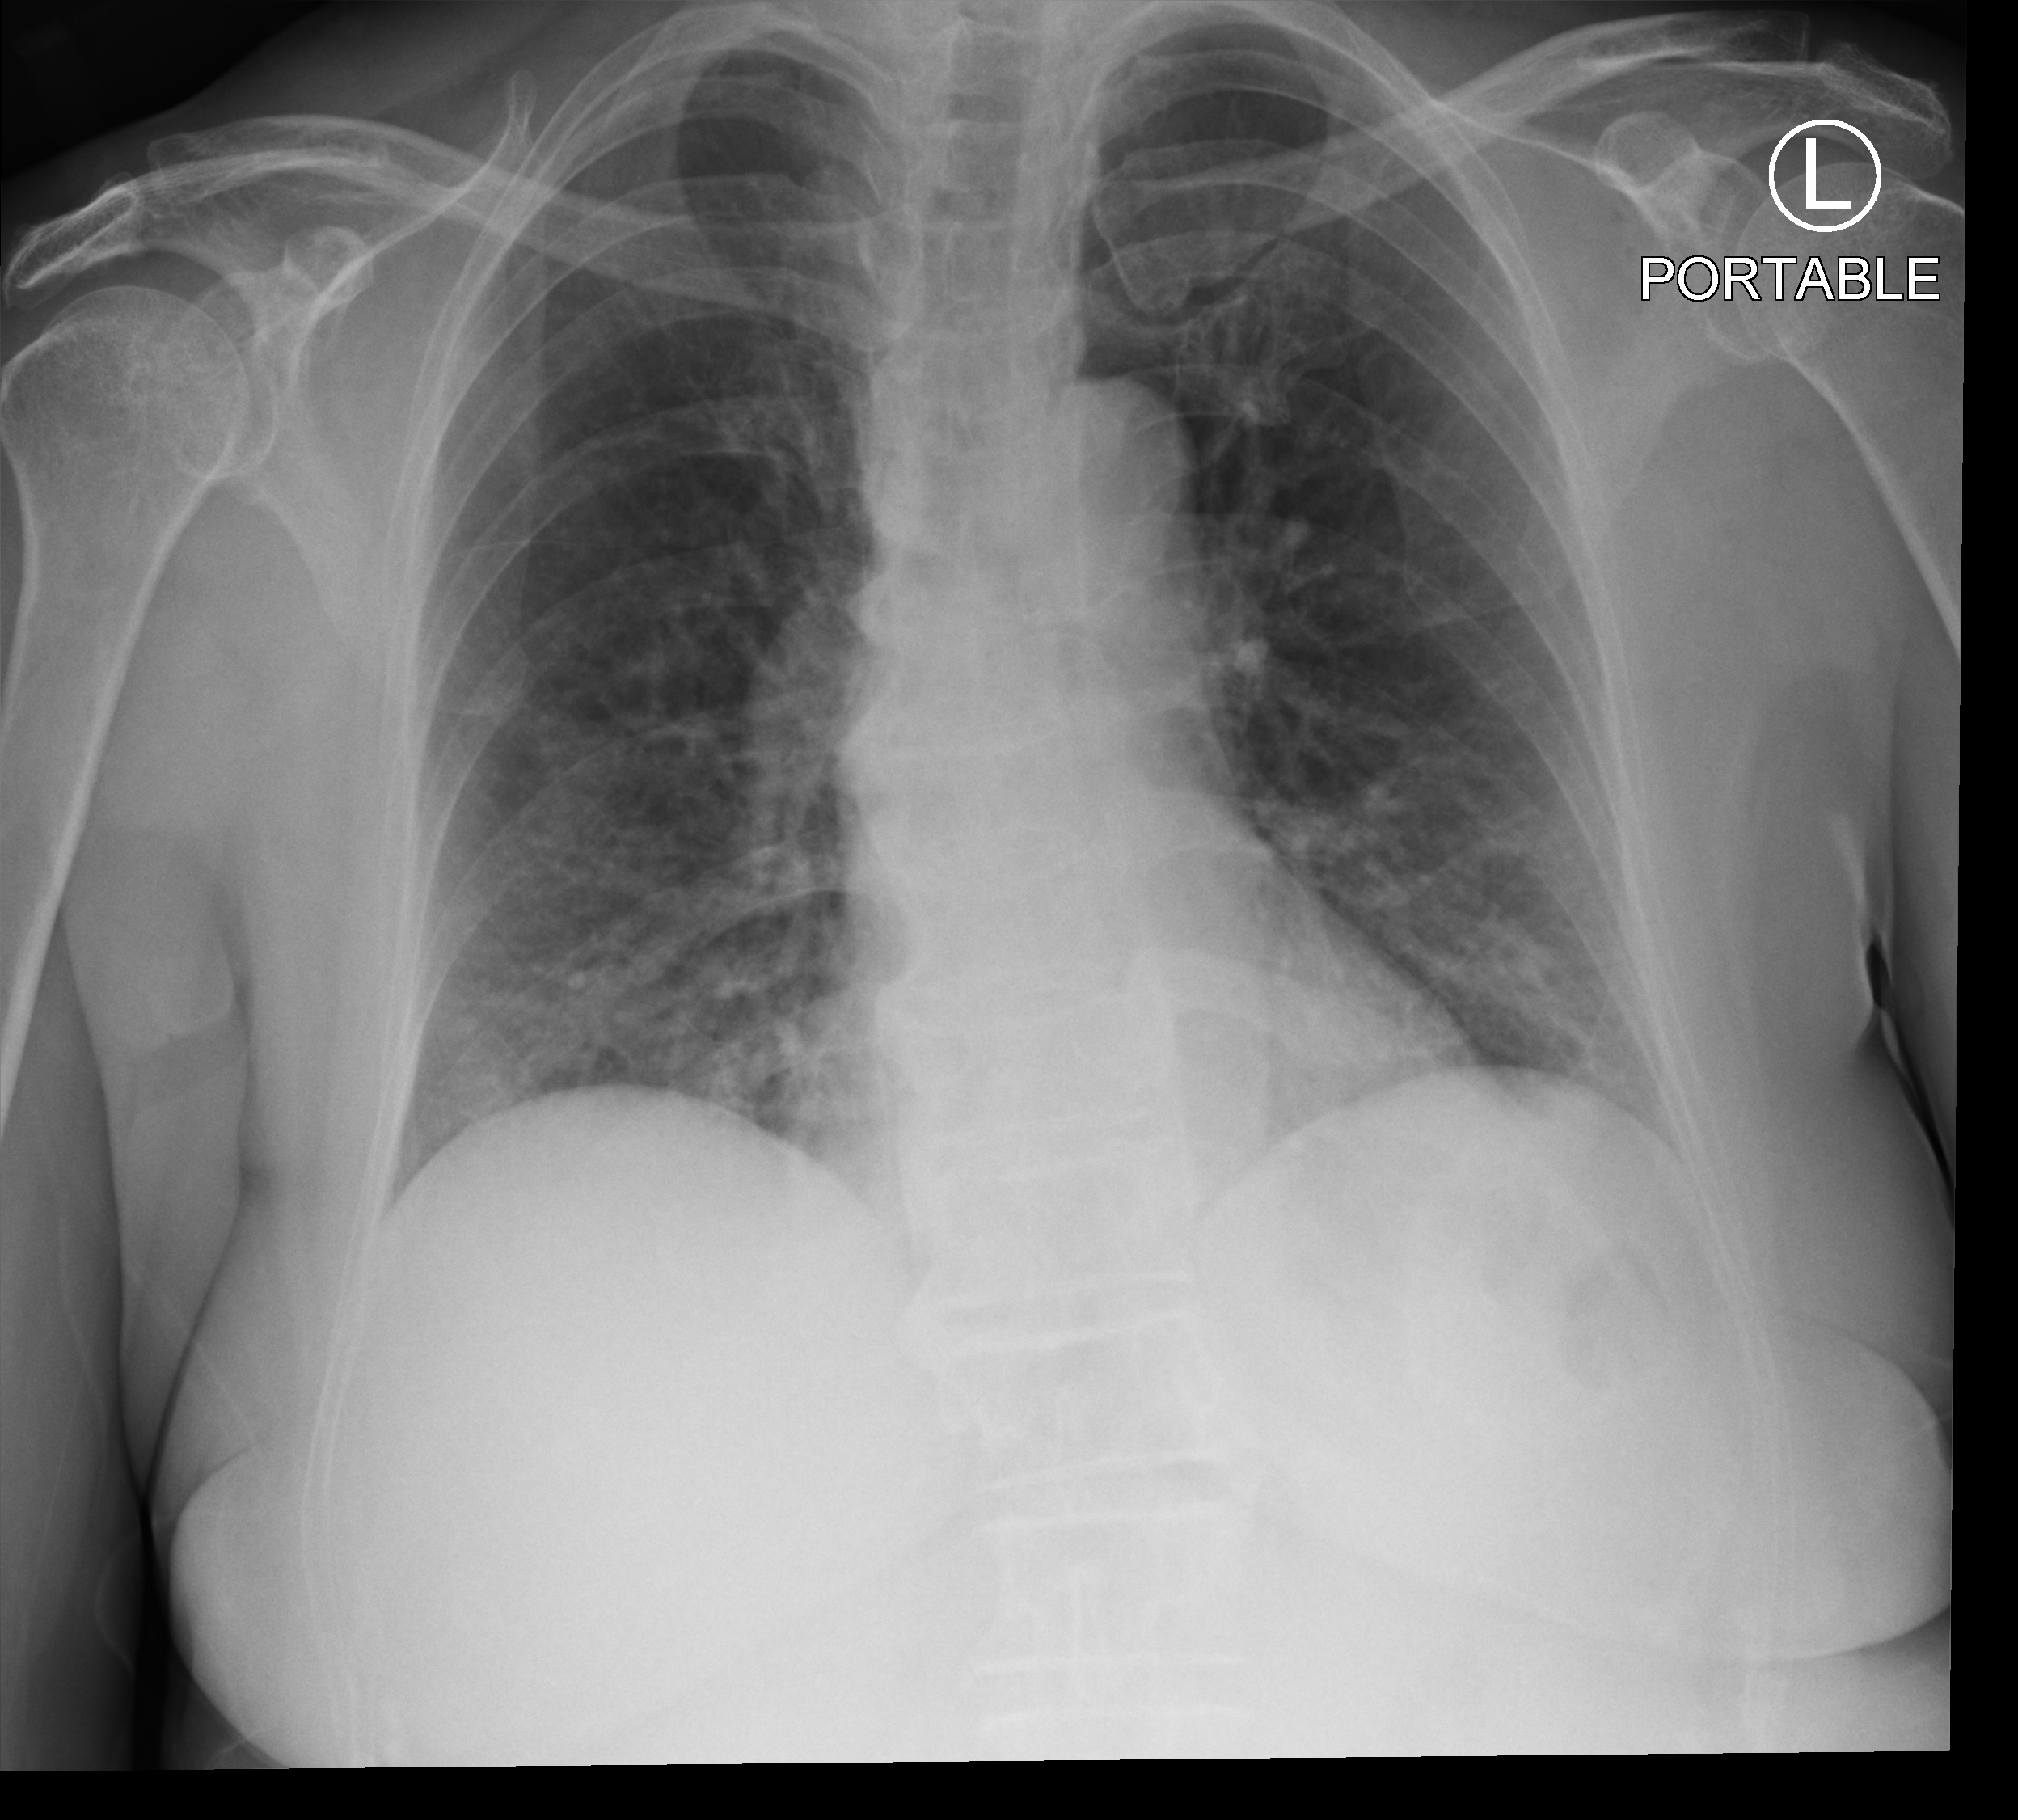
Bedside chest radiograph (computed radiography); anteroposterior (AP) projection. Female patient hospitalised with COVID-19, age 60–74 years.
From the hospital-stay record, not from the radiograph (when in the stay this image was taken is not recorded):
- length of hospital stay: 6 days
- admitted to intensive care during this hospital stay: no
- mechanically ventilated during this hospital stay: no